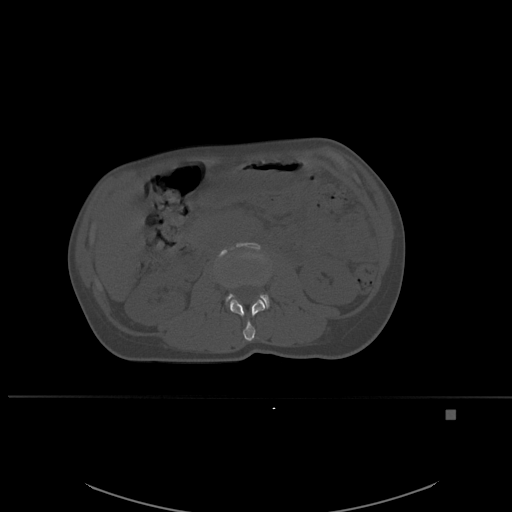
CT including the spine, one axial slice. Slice 226 of 537 in the series (ordered by position). Bone window (W 1800 / L 400 HU). 512 × 512 image matrix. Female patient, age 45 years. From the clinical record (not read from this slice): primary cancer: lung.
Outlined on this slice (semi-automatic segmentation, software-assisted and operator-edited):
- L2 vertebra: box from (x=226, y=285) to (x=266, y=341) px
- L3 vertebra: (x=215, y=242)–(x=270, y=309)